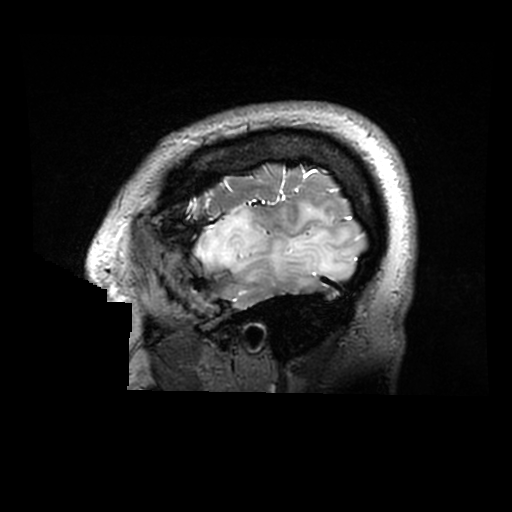
Brain MRI from a brain-tumour surgery series, one sagittal slice; position 249 of 320 along the scan axis; 512 × 512 image matrix, field of view 240 × 240 mm. From the clinical record (not read from this slice): histopathology: Astrocytoma; WHO grade: 2; IDH mutation: yes.
Outlined on this slice (outlined manually by an expert reader):
- tumour: bounding box <196,202,351,286> (left, top, right, bottom; pixels)